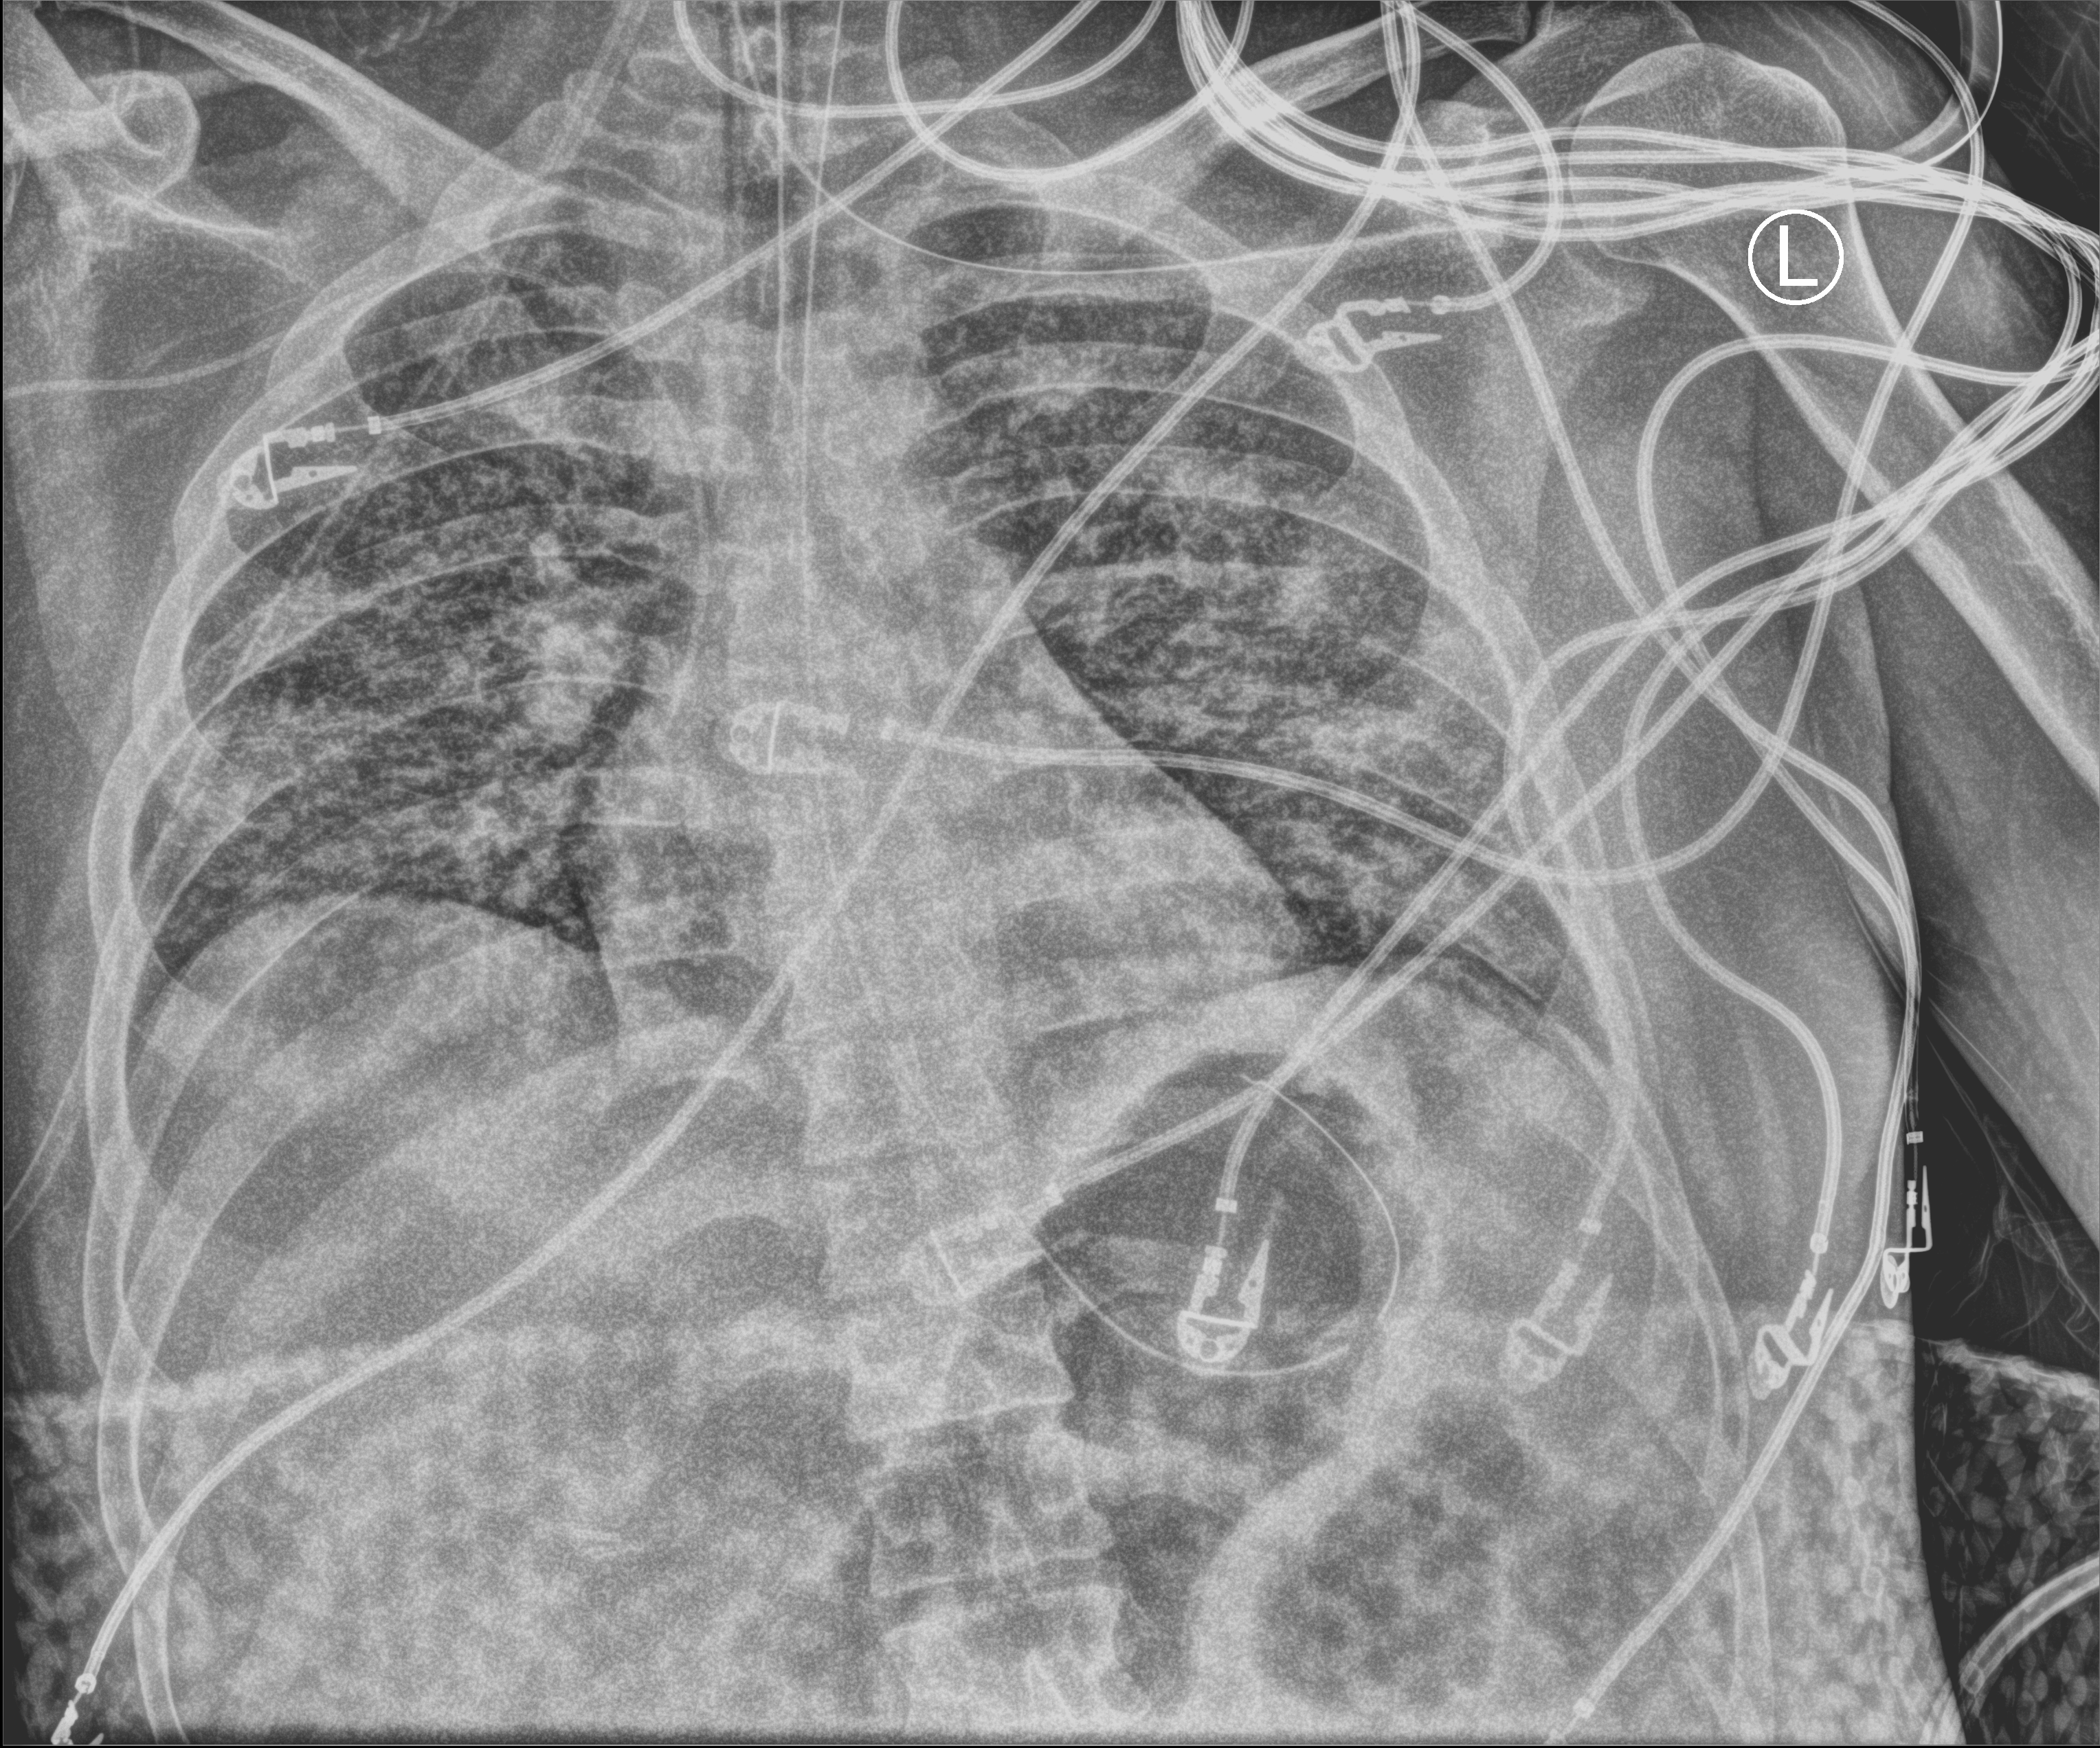
Chest X-ray (portable); anteroposterior (AP) projection. Male patient hospitalised with COVID-19, age 18–59 years.
Admission-level facts for this patient (not findings on this image; timing relative to this image not recorded): admitted to intensive care during this hospital stay: yes.